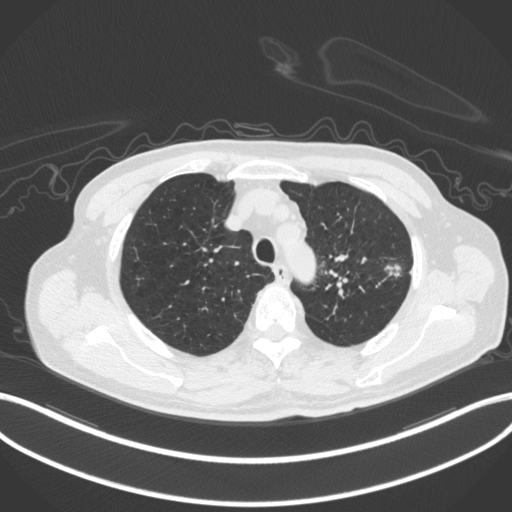
Chest CT, one axial slice. Slice 350 of 420 in the series (ordered by position). Reconstruction kernel B31f. Lung window (W 1500 / L -600 HU). 1 mm slice thickness. 512 × 512 image matrix, field of view 400 × 400 mm. Male patient, age 77 years. From the clinical record (not read from this slice): clinical TNM (as recorded): T3 N1 M0.
Outlined on this slice (bounding box drawn by a radiologist):
- lung tumour (recorded histology: adenocarcinoma): bounding box <383,261,405,278> (left, top, right, bottom; pixels)